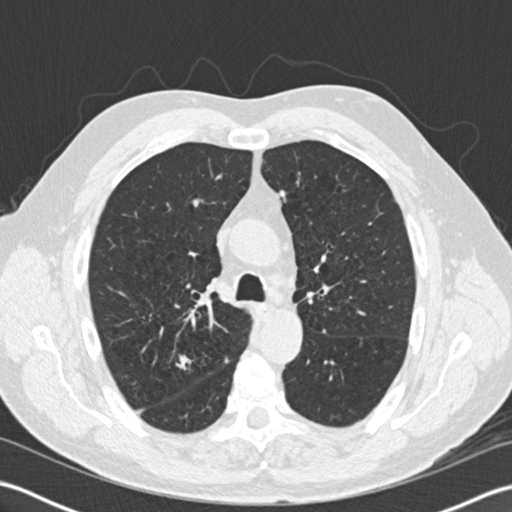
Axial slice from a low-dose chest CT screening exam. Second screening round (one year after baseline). Lung window (W 1500 / L -600 HU). 2 mm slice thickness. 120 kVp. Slice 57 of 204 in the series. Male, age 65 years at enrolment. Former smoker at enrolment.
Lesion marked by an expert reader, bounding box [x1, y1, x2, y2] px = [159, 346, 204, 384]. The screening reader recorded 6 non-calcified nodules or masses ≥4 mm on this exam (right upper lobe, left upper lobe, left upper lobe, right upper lobe, left upper lobe, right upper lobe); which of them this box marks is not recorded. Official screen result: positive, other.